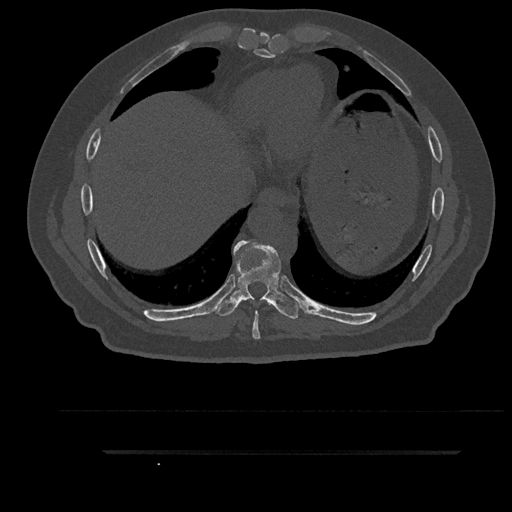
CT including the spine, one axial slice; slice 441 of 797 in the series (ordered by position); reconstruction kernel Br40s/3; bone window (W 1800 / L 400 HU); 0.5 mm slice thickness; 512 × 512 image matrix, field of view 432 × 432 mm. Patient: male, 63 years. From the clinical record (not read from this slice): primary cancer: renal; vertebrae with lytic lesions (as recorded): T8.
Structures marked on this image (semi-automatic segmentation, software-assisted and operator-edited):
- T8 vertebra: bounding box <234,241,273,339> (left, top, right, bottom; pixels)
- T9 vertebra: <212,240,299,319>